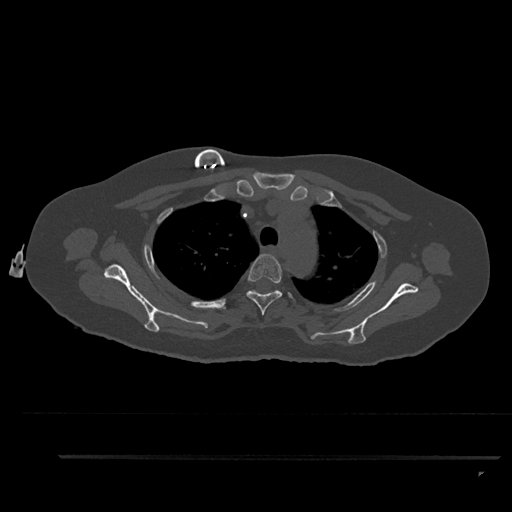
CT including the spine, one axial slice. Slice 679 of 797 in the series (ordered by position). Reconstruction kernel Br40s/3. 120 kVp. Bone window (W 1800 / L 400 HU). 0.5 mm slice thickness. 512 × 512 image matrix. Patient: female, 44 years. Case-level facts recorded for this patient, not image findings: primary cancer: renal; vertebrae with lytic lesions (as recorded): L1.
Outlined on this slice (semi-automatic segmentation, software-assisted and operator-edited):
- T3 vertebra: bounding box (x1, y1, x2, y2) in pixels: (246, 254, 293, 315)